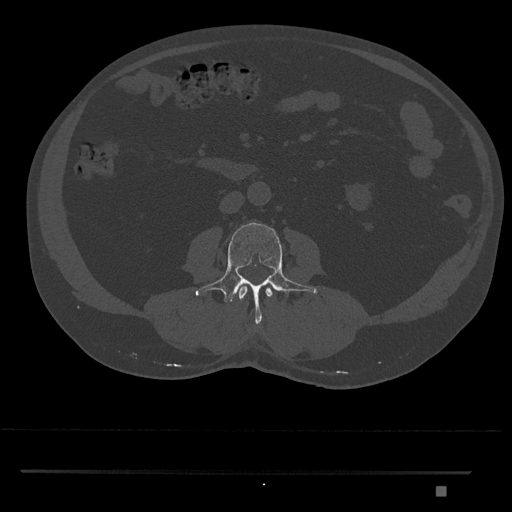
CT including the spine, one axial slice. Position 690 of 1134 along the scan axis. 120 kVp. Bone window (W 1800 / L 400 HU). 512 × 512 image matrix. Male patient, age 65 years. Case-level facts recorded for this patient, not image findings: primary cancer: prostate.
Annotated regions visible in this slice (semi-automatically segmented with operator editing):
- L2 vertebra: bounding box <238,285,273,300> (left, top, right, bottom; pixels)
- L3 vertebra: <195,222,318,325>